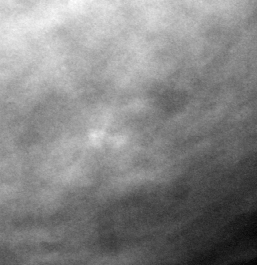
Region of interest cut from a scanned film mammogram (one marked finding), left breast, CC view, BI-RADS breast density category 3 (scale 1–4).
Marked abnormality: calcifications, morphology dystrophic, distribution clustered; BI-RADS assessment category 3; subtlety rating 3 on a 1 (subtle) to 5 (obvious) scale; pathology result (as recorded, not read from the image): benign.